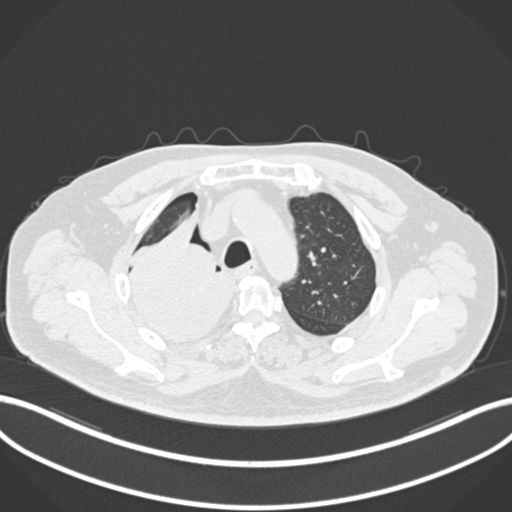
Chest CT, one axial slice. Position 165 of 218 along the scan axis. Reconstruction kernel B30f. Lung window (W 1500 / L -600 HU). 512 × 512 image matrix, field of view 400 × 400 mm. Male patient, age 68 years. From the clinical record (not read from this slice): clinical TNM (as recorded): T2a N0 M0.
Outlined on this slice (bounding box drawn by a radiologist):
- lung tumour (recorded histology: adenocarcinoma): bounding box [x1, y1, x2, y2] px = [127, 229, 234, 345]